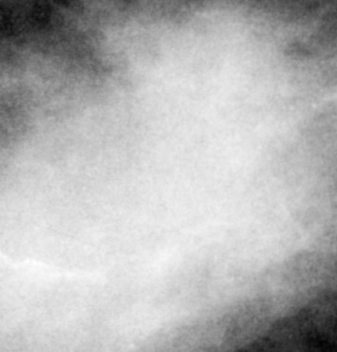
Region of interest cut from a scanned film mammogram (one marked finding), left breast, CC view, BI-RADS breast density category 2 (scale 1–4).
Finding: mass, shape oval, margins ill defined; BI-RADS assessment category 4; subtlety rating 4 on a 1 (subtle) to 5 (obvious) scale; pathology result (as recorded, not read from the image): malignant.